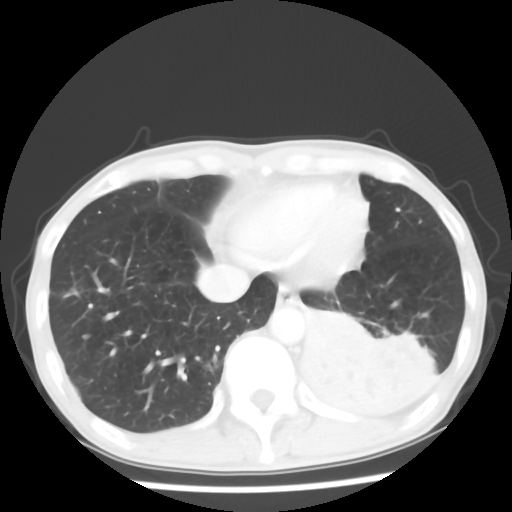
Chest CT, one axial slice; position 14 of 64 along the scan axis; reconstruction kernel STANDARD; lung window (W 1500 / L -600 HU); 5 mm slice thickness; 512 × 512 image matrix, field of view 313 × 313 mm. Patient: male, 68 years. Case-level facts recorded for this patient, not image findings: clinical TNM (as recorded): T4 N0 M0.
Outlined on this slice (rectangle marked by the reading radiologist):
- lung tumour (recorded histology: squamous cell carcinoma): bounding box (x1, y1, x2, y2) in pixels: (307, 315, 440, 424)